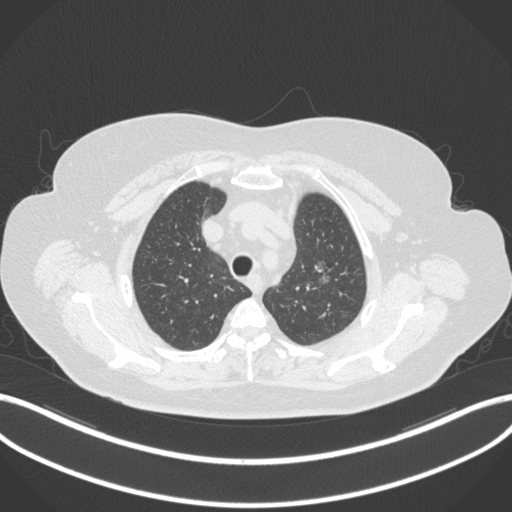
Chest CT, one axial slice; slice 272 of 310 in the series (ordered by position); 120 kVp; lung window (W 1500 / L -600 HU); 1 mm slice thickness; 512 × 512 image matrix, field of view 400 × 400 mm. Female patient, age 70 years. Case-level facts recorded for this patient, not image findings: clinical TNM (as recorded): T1c N0 M0.
Outlined on this slice (bounding box drawn by a radiologist):
- lung tumour (recorded histology: adenocarcinoma): box from (x=313, y=260) to (x=332, y=287) px